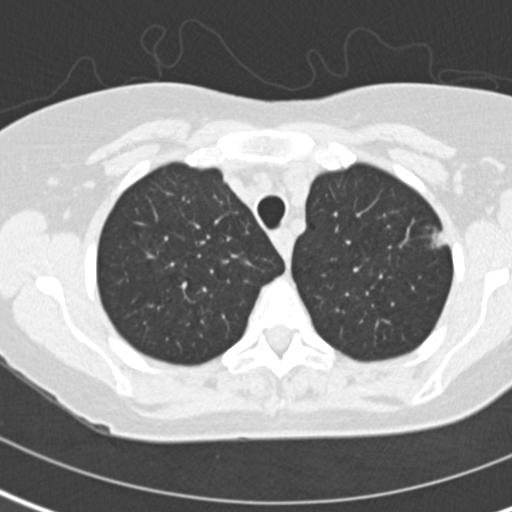
Low-dose screening chest CT, axial slice; second screening round (one year after baseline); lung window (W 1500 / L -600 HU); standard (soft-tissue) reconstruction kernel (B30f); slice 26 of 141 in the series; 512 × 512 image matrix. Female, age 60 years at enrolment. Former smoker at enrolment.
Expert reader's lesion annotation, box from (x=415, y=224) to (x=463, y=264) px. The screening reader recorded 2 non-calcified nodules or masses ≥4 mm on this exam (left upper lobe, left upper lobe); which of them this box marks is not recorded. Official screen result: positive, change unspecified: nodule(s) >= 4 mm or enlarging nodule(s), mass(es), or other non-specific abnormalities suspicious for lung cancer. Participant outcome: lung cancer diagnosed 116 days after this screen — adenocarcinoma, NOS, left upper lobe, moderately differentiated (G2), stage IA (AJCC 6th edition), 11 mm at pathology.